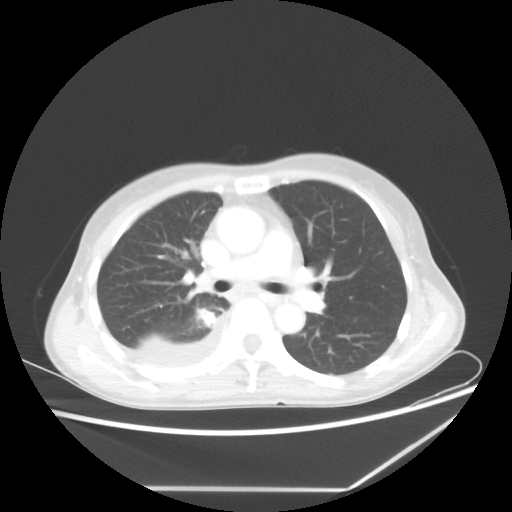
Chest CT, one axial slice. Position 37 of 60 along the scan axis. Lung window (W 1500 / L -600 HU). 512 × 512 image matrix, field of view 364 × 364 mm. Female patient, age 59 years. Case-level facts recorded for this patient, not image findings: clinical TNM (as recorded): T1c N1 M1.
Structures marked on this image (rectangle marked by the reading radiologist):
- lung tumour (recorded histology: adenocarcinoma): bounding box [x1, y1, x2, y2] px = [192, 304, 219, 330]